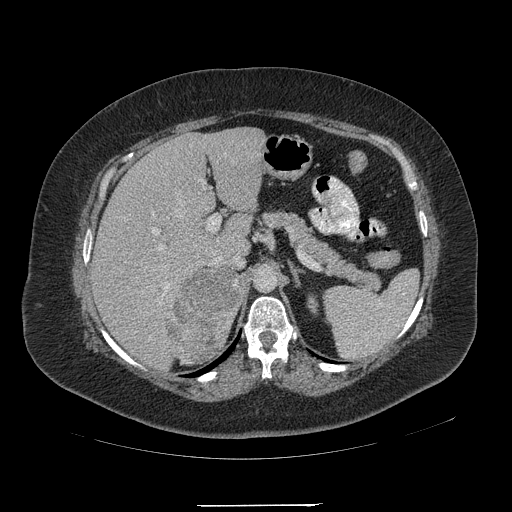
Contrast-enhanced abdominal CT, one axial slice. Position 140 of 217 along the scan axis. Reconstruction kernel STANDARD. Intravenous contrast given. Soft-tissue window (W 400 / L 40 HU). 1.25 mm slice thickness. 512 × 512 image matrix, field of view 453 × 453 mm. Female patient, age 55 years. Case-level facts recorded for this patient, not image findings: diagnosis: adrenocortical carcinoma; tumour side: right adrenal; tumour size at pathology: 11 cm; Ki-67 index: 20 %; stage (as recorded): 2.
Structures marked on this image (semi-automatic segmentation, software-assisted and operator-edited):
- mass: box from (x=167, y=267) to (x=241, y=360) px